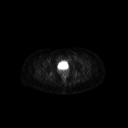
FDG PET of an extremity soft-tissue mass (from a PET/CT study), one axial slice. Position 57 of 267 along the scan axis. 128 × 128 image matrix. Patient: female, 47 years. From the clinical record (not read from this slice): histological type: myxofibrosarcoma; grade: intermediate; site of the primary tumour: left thigh.
Annotated regions visible in this slice (expert contour drawn on MRI and transferred to this co-registered scan by the dataset authors):
- gross tumour volume including surrounding oedema: box from (x=68, y=58) to (x=82, y=63) px